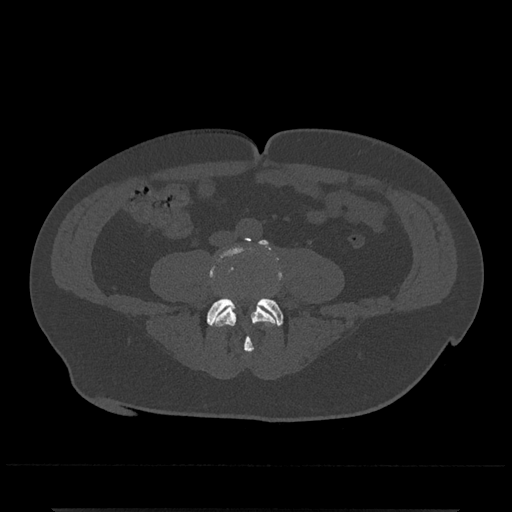
CT including the spine, one axial slice. Slice 123 of 797 in the series (ordered by position). 120 kVp. Bone window (W 1800 / L 400 HU). 0.5 mm slice thickness. 512 × 512 image matrix, field of view 393 × 393 mm. Patient: male, 67 years. From the clinical record (not read from this slice): primary cancer: prostate.
Structures marked on this image (semi-automatic segmentation, software-assisted and operator-edited):
- L4 vertebra: box from (x=209, y=240) to (x=283, y=353) px
- L5 vertebra: (x=207, y=297)–(x=283, y=326)